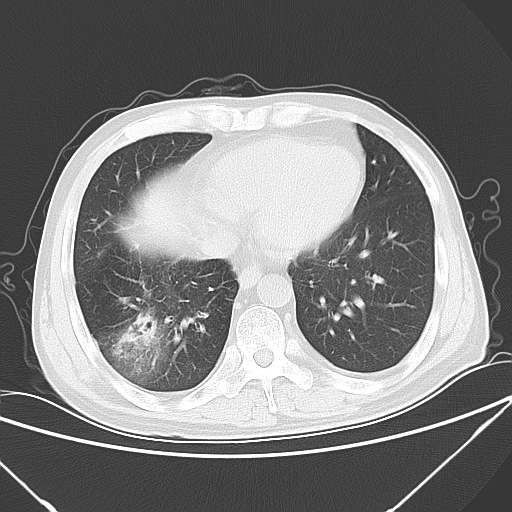
Chest CT, one axial slice; slice 21 of 57 in the series (ordered by position); lung window (W 1500 / L -600 HU); 5 mm slice thickness; 512 × 512 image matrix. Male patient, age 54 years. From the clinical record (not read from this slice): clinical TNM (as recorded): T2 N1 M0; histopathological grade: G3.
Outlined on this slice (rectangle marked by the reading radiologist):
- lung tumour (recorded histology: adenocarcinoma): box from (x=109, y=310) to (x=160, y=359) px